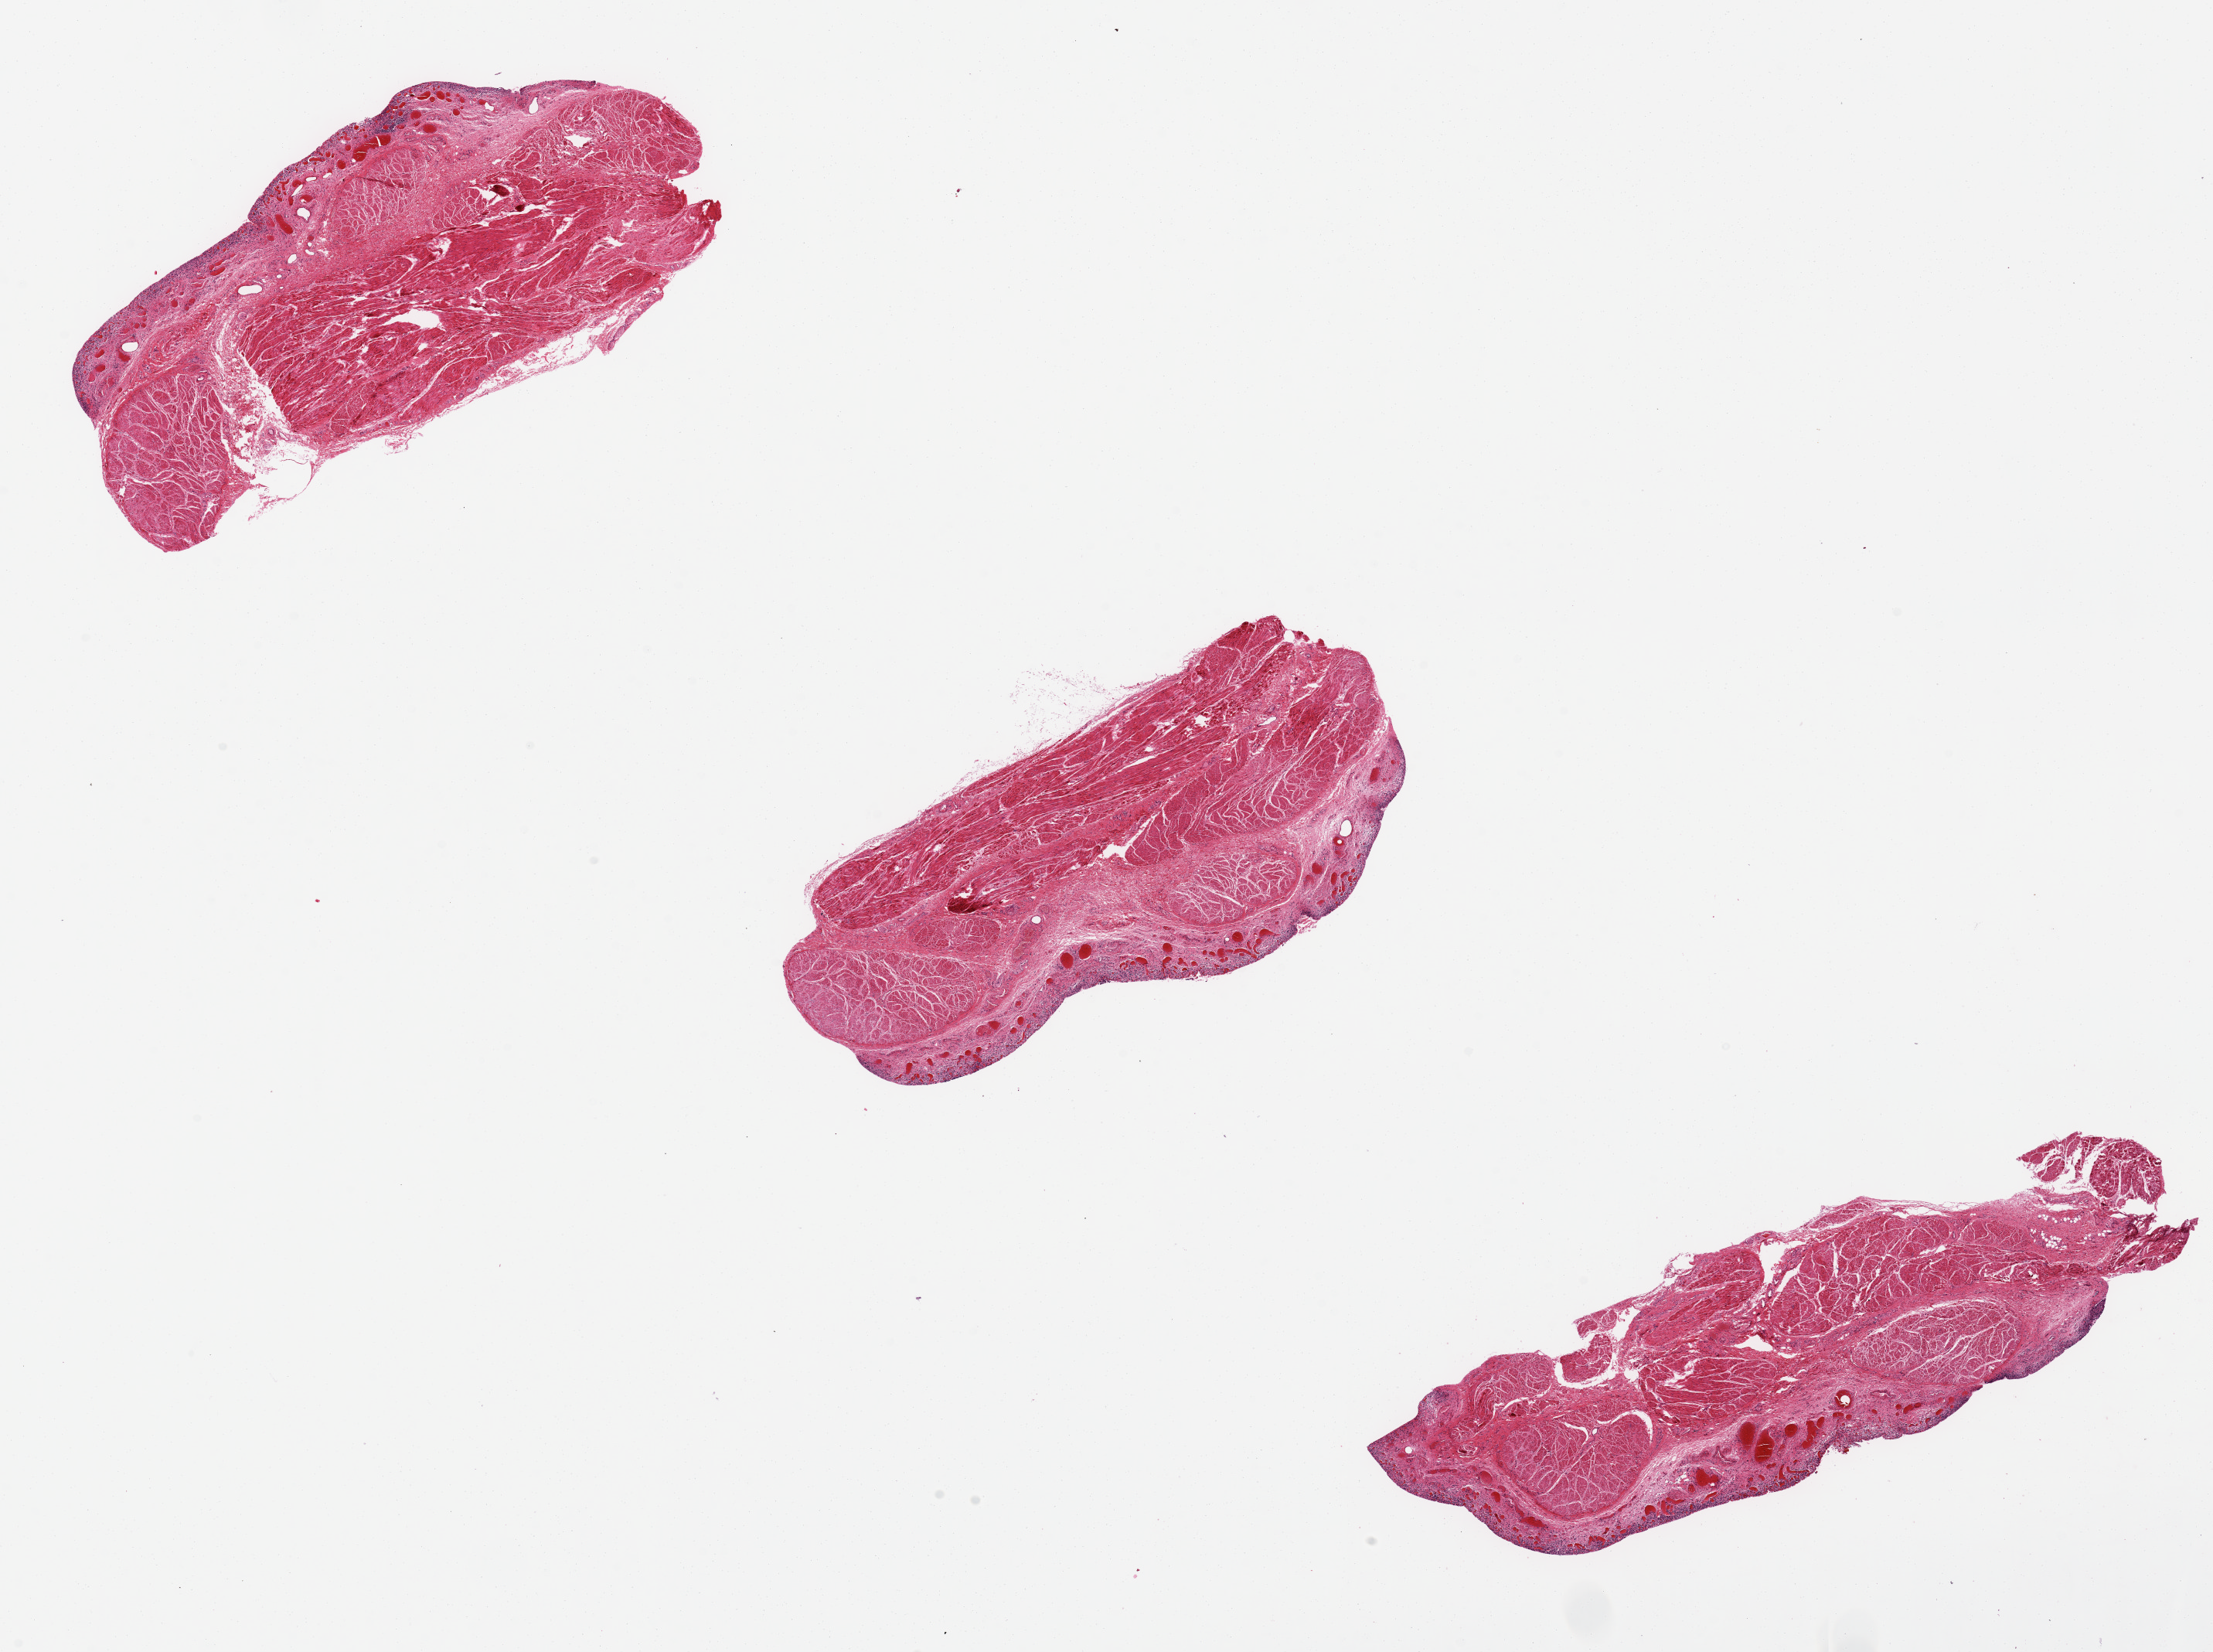
Whole-slide image, H&E stain — low-resolution overview of the scanned area, about 22.6 x 16.9 mm; PAXgene-fixed paraffin-embedded (PFPE) section; section of urinary bladder (target tissue); tissue donor sample.
- pathologist's review note for this sample: Mucosa completely sloughed. 3 pieces 6.7x 2.4mm